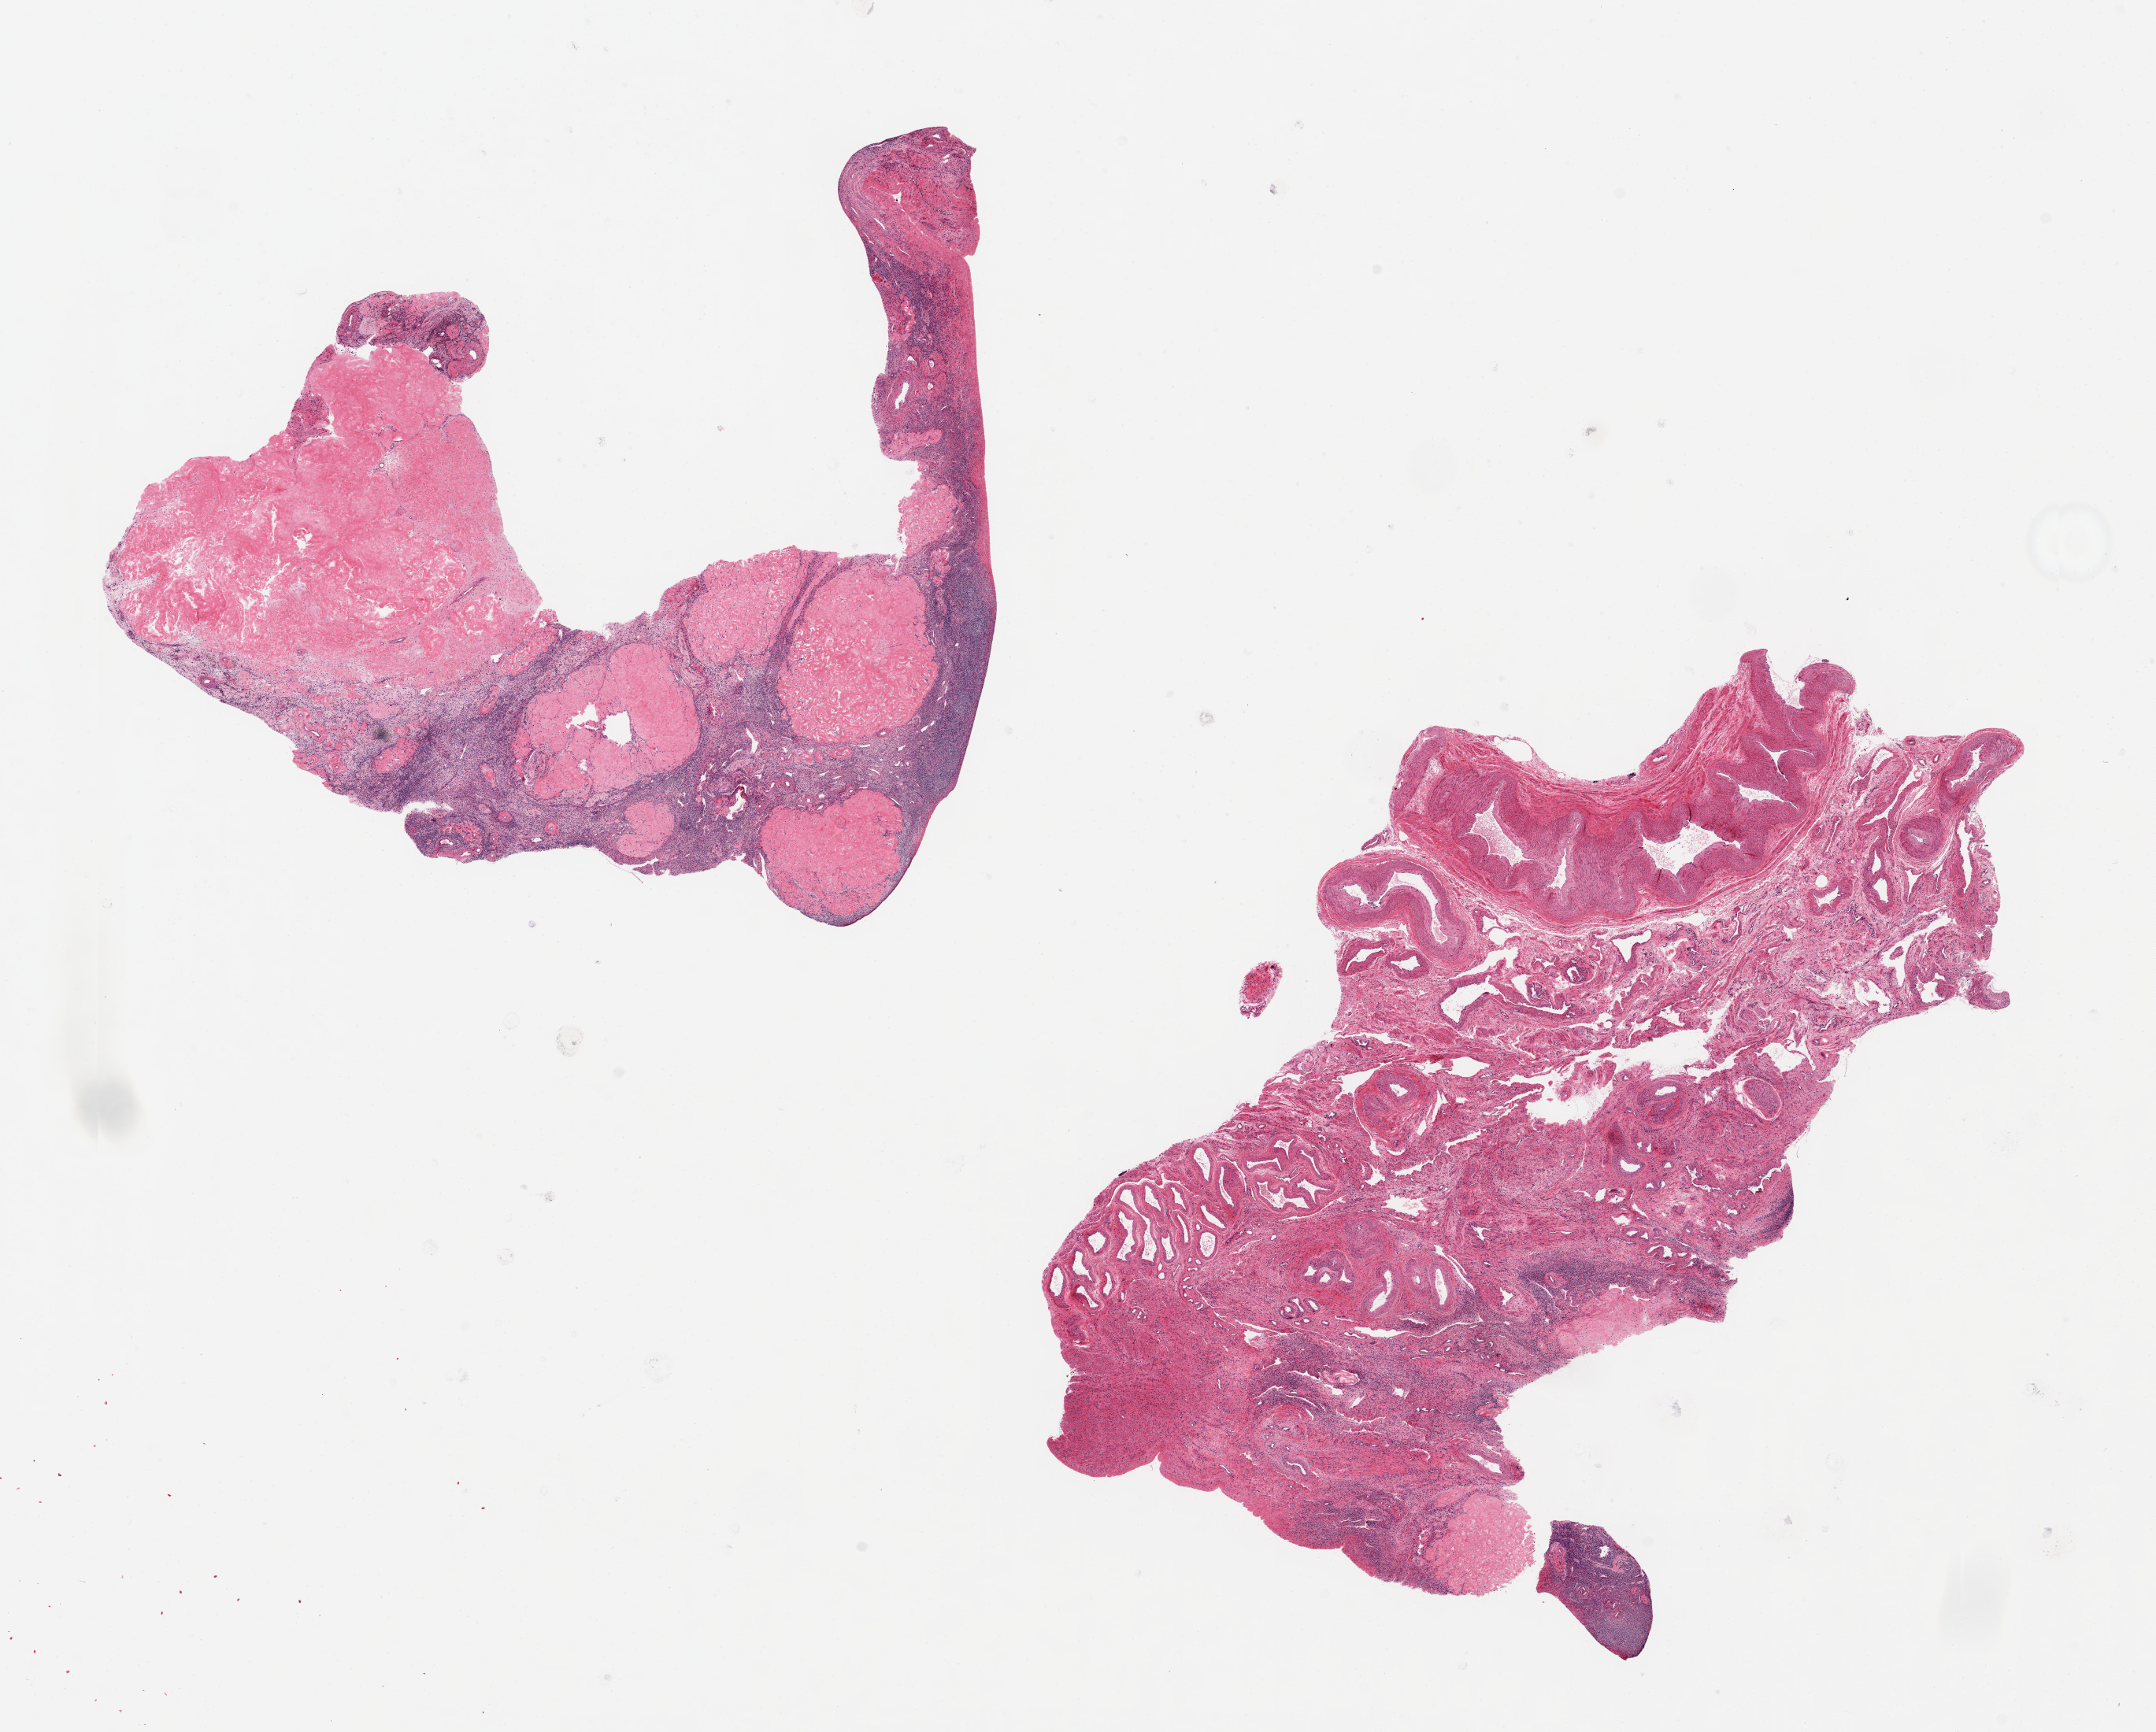
Hematoxylin and eosin (H&E) whole-slide image, low-resolution overview of the scanned area, about 21.7 x 17.4 mm, PAXgene-fixed, paraffin-embedded tissue, sampled site (target tissue): ovary, tissue donor sample. Donor: female.
- pathologist's review note for this sample: 2 aliquots, ~9x6mm. Prominent corpora albicantia, no visible oocytes noted